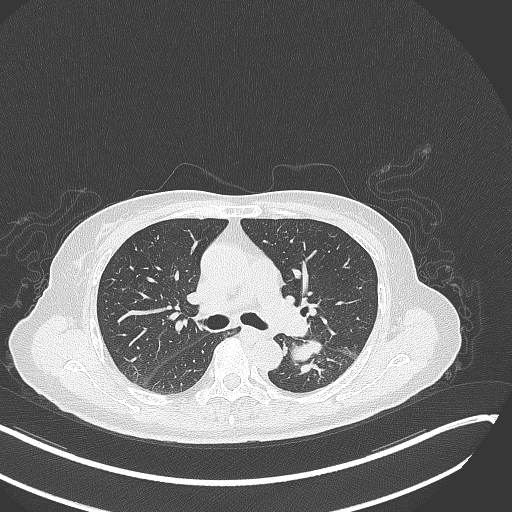
Chest CT, one axial slice; slice 176 of 342 in the series (ordered by position); lung window (W 1500 / L -600 HU); 1 mm slice thickness; 512 × 512 image matrix, field of view 400 × 400 mm. Patient: female, 64 years. Case-level facts recorded for this patient, not image findings: clinical TNM (as recorded): T3 N1 M1; histopathological grade: G3.
Outlined on this slice (bounding box drawn by a radiologist):
- lung tumour (recorded histology: small cell carcinoma): bounding box <286,332,327,361> (left, top, right, bottom; pixels)